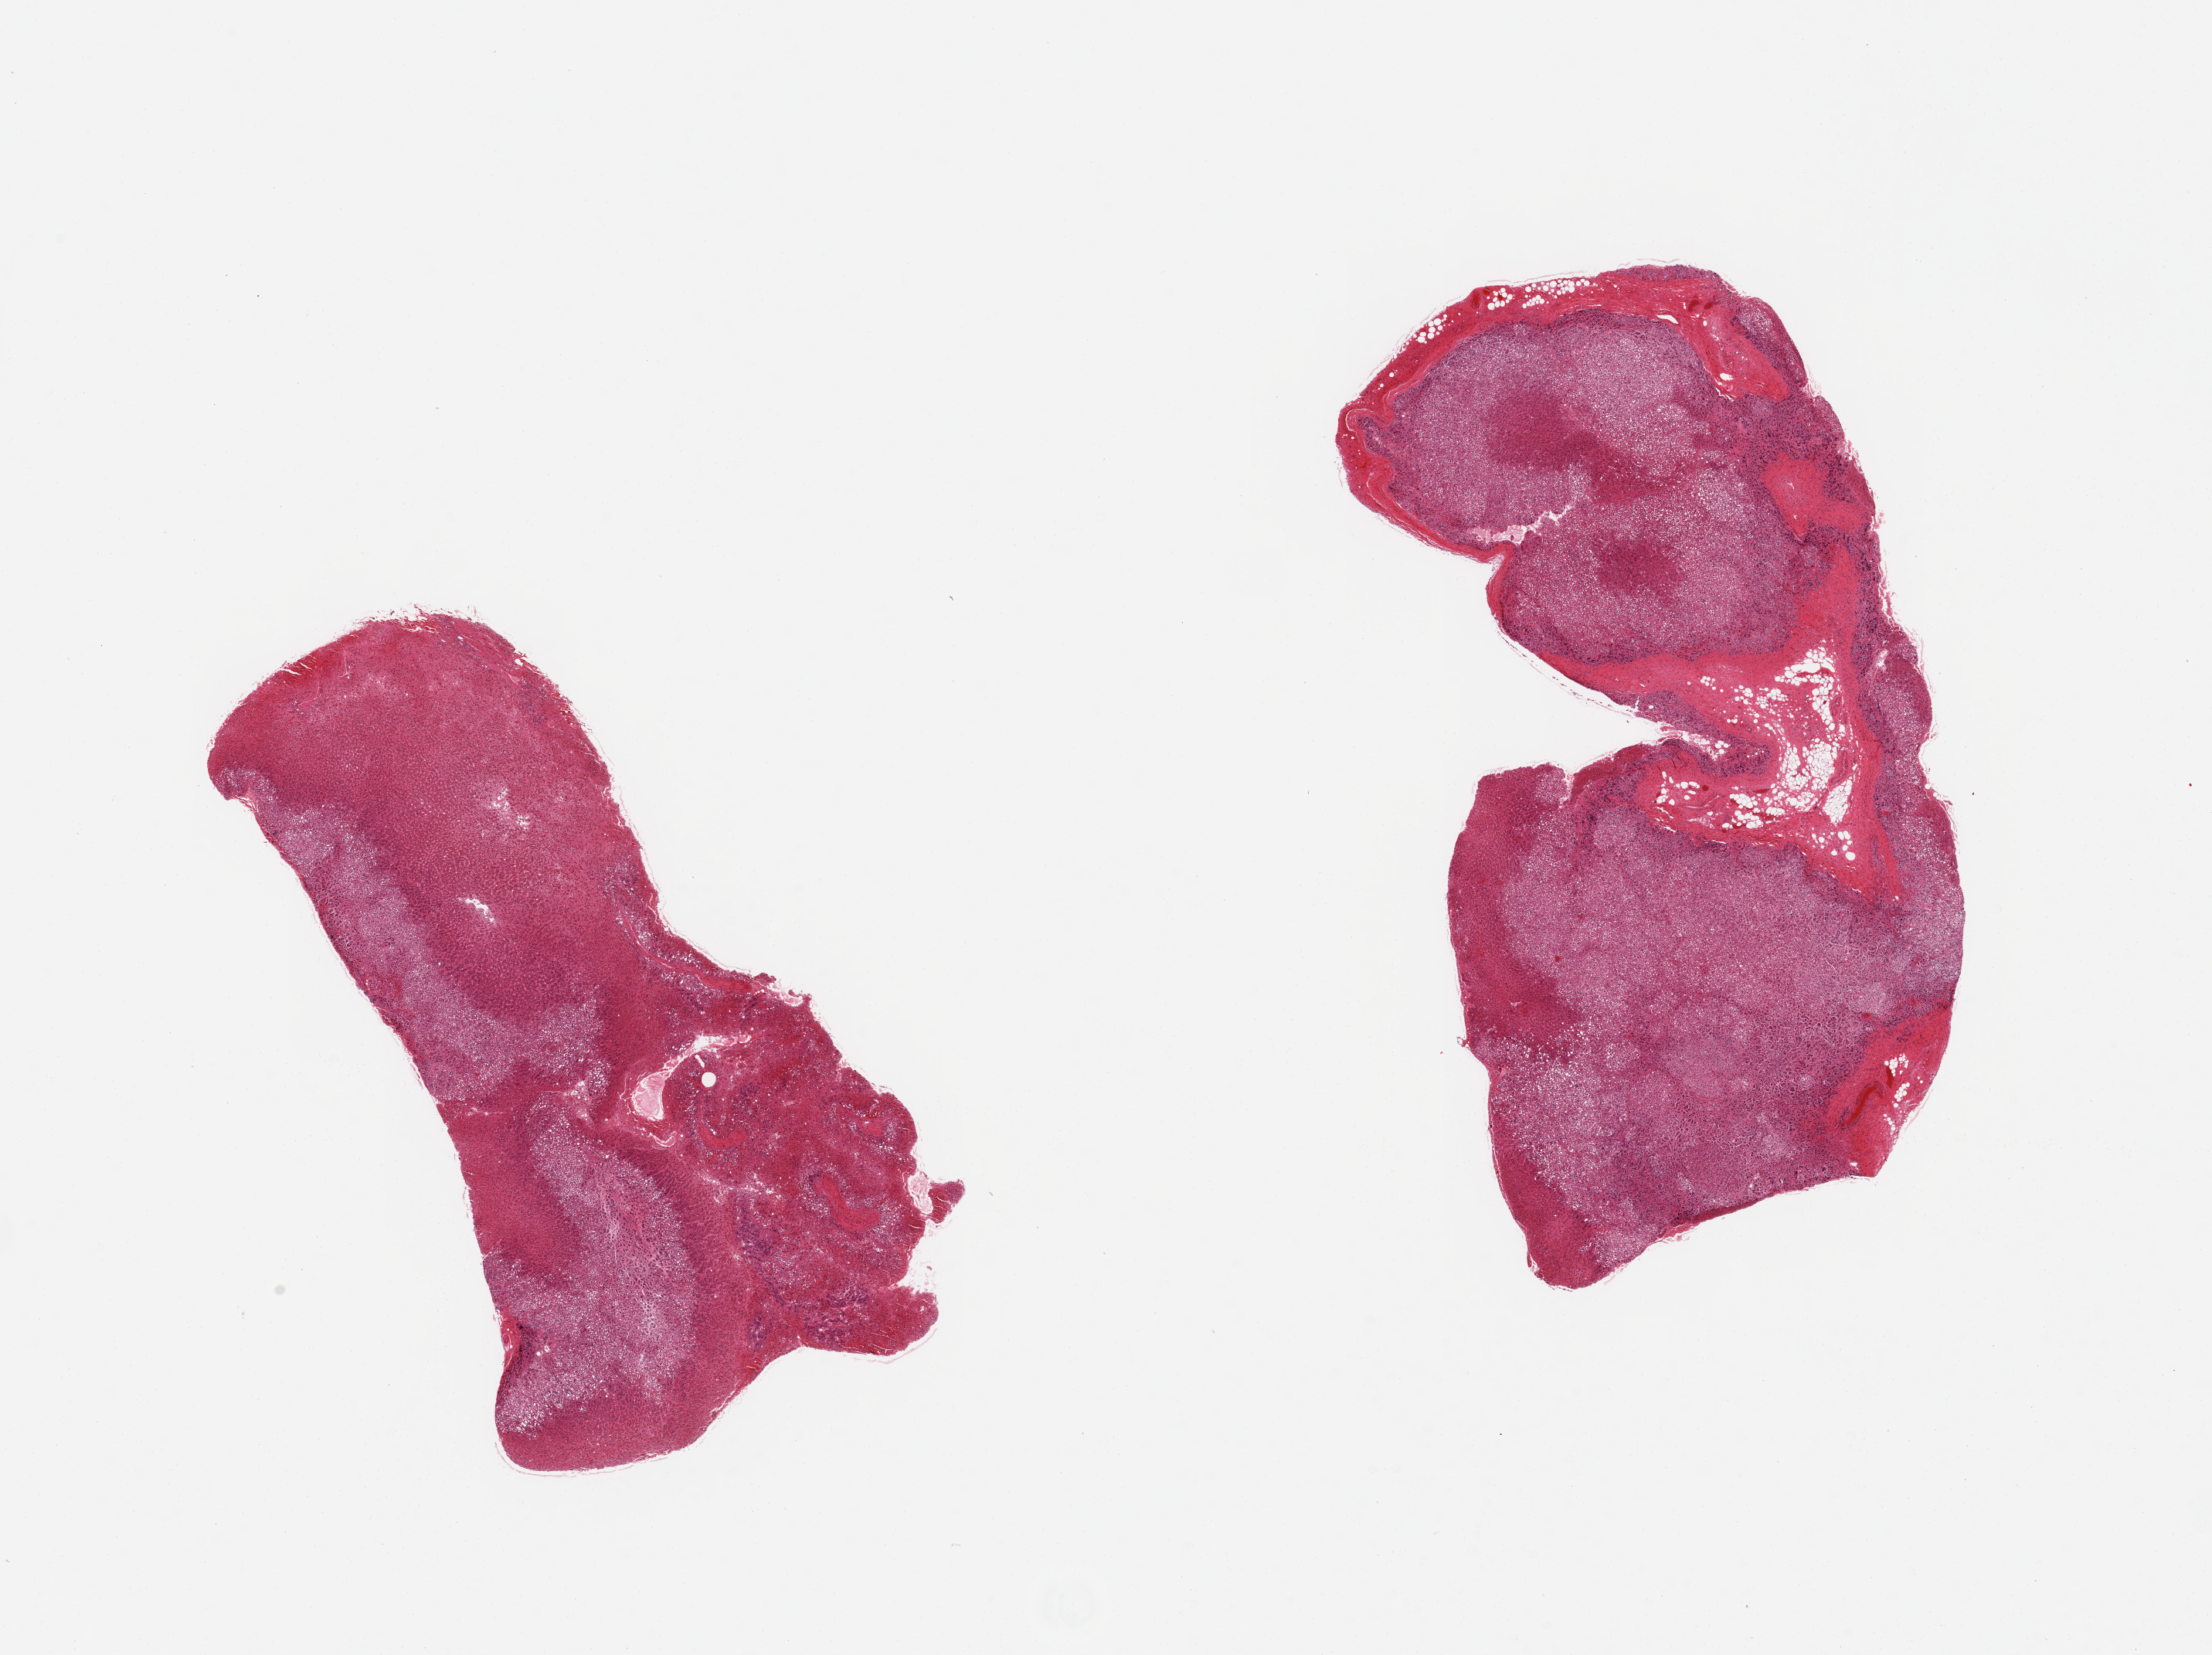
Digitized haematoxylin and eosin-stained section, brightfield, low-resolution overview of the scanned area, about 22.6 x 16.9 mm (acquisition: 20x scan). PAXgene-fixed paraffin-embedded (PFPE) section. Target tissue: adrenal gland. Tissue donor sample.
• pathologist's review note for this sample: 2 pieces; 10% internal fat but generally well trimmed